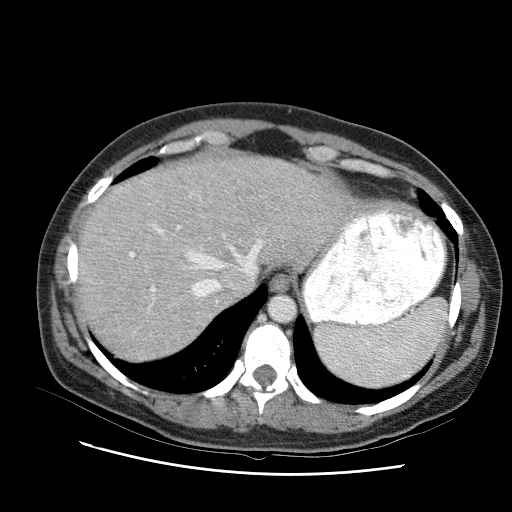
Contrast-enhanced abdominal CT (liver protocol), one axial slice; slice 76 of 95 in the series (ordered by position); 120 kVp; one of 2 acquisitions stored at this slice position; soft-tissue window (W 400 / L 40 HU); 2.5 mm slice thickness; 512 × 512 image matrix, field of view 360 × 360 mm. From the clinical record (not read from this slice): diagnosis: hepatocellular carcinoma (patient treated with transarterial chemoembolisation; whether this scan precedes or follows treatment is not stated here); TNM stage (as recorded): Stage-I.
Structures marked on this image (semi-automatic segmentation, software-assisted and operator-edited):
- liver parenchyma outside the tumour (the mass and vessels are separate outlines, so this box may not span the whole liver): bounding box [x1, y1, x2, y2] px = [78, 148, 324, 340]
- liver vessels: [107, 221, 238, 302]